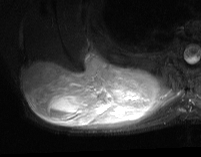
MRI of an extremity soft-tissue mass, one axial slice; slice 31 of 74 in the series (ordered by position); STIR; MR volume resampled by the dataset authors to the PET/CT grid (not the native acquisition matrix); 3.27 mm slice thickness; 201 × 157 image matrix, field of view 196 × 153 mm. Male patient. Case-level facts recorded for this patient, not image findings: histological type: pleiomorphic spindle cell undifferentiated; grade: high; site of the primary tumour: right parascapusular.
Outlined on this slice (expert contour drawn on MRI and transferred to this co-registered scan by the dataset authors):
- gross tumour volume including surrounding oedema: box from (x=24, y=52) to (x=178, y=131) px
- gross tumour volume (mass): (x=24, y=52)–(x=159, y=127)